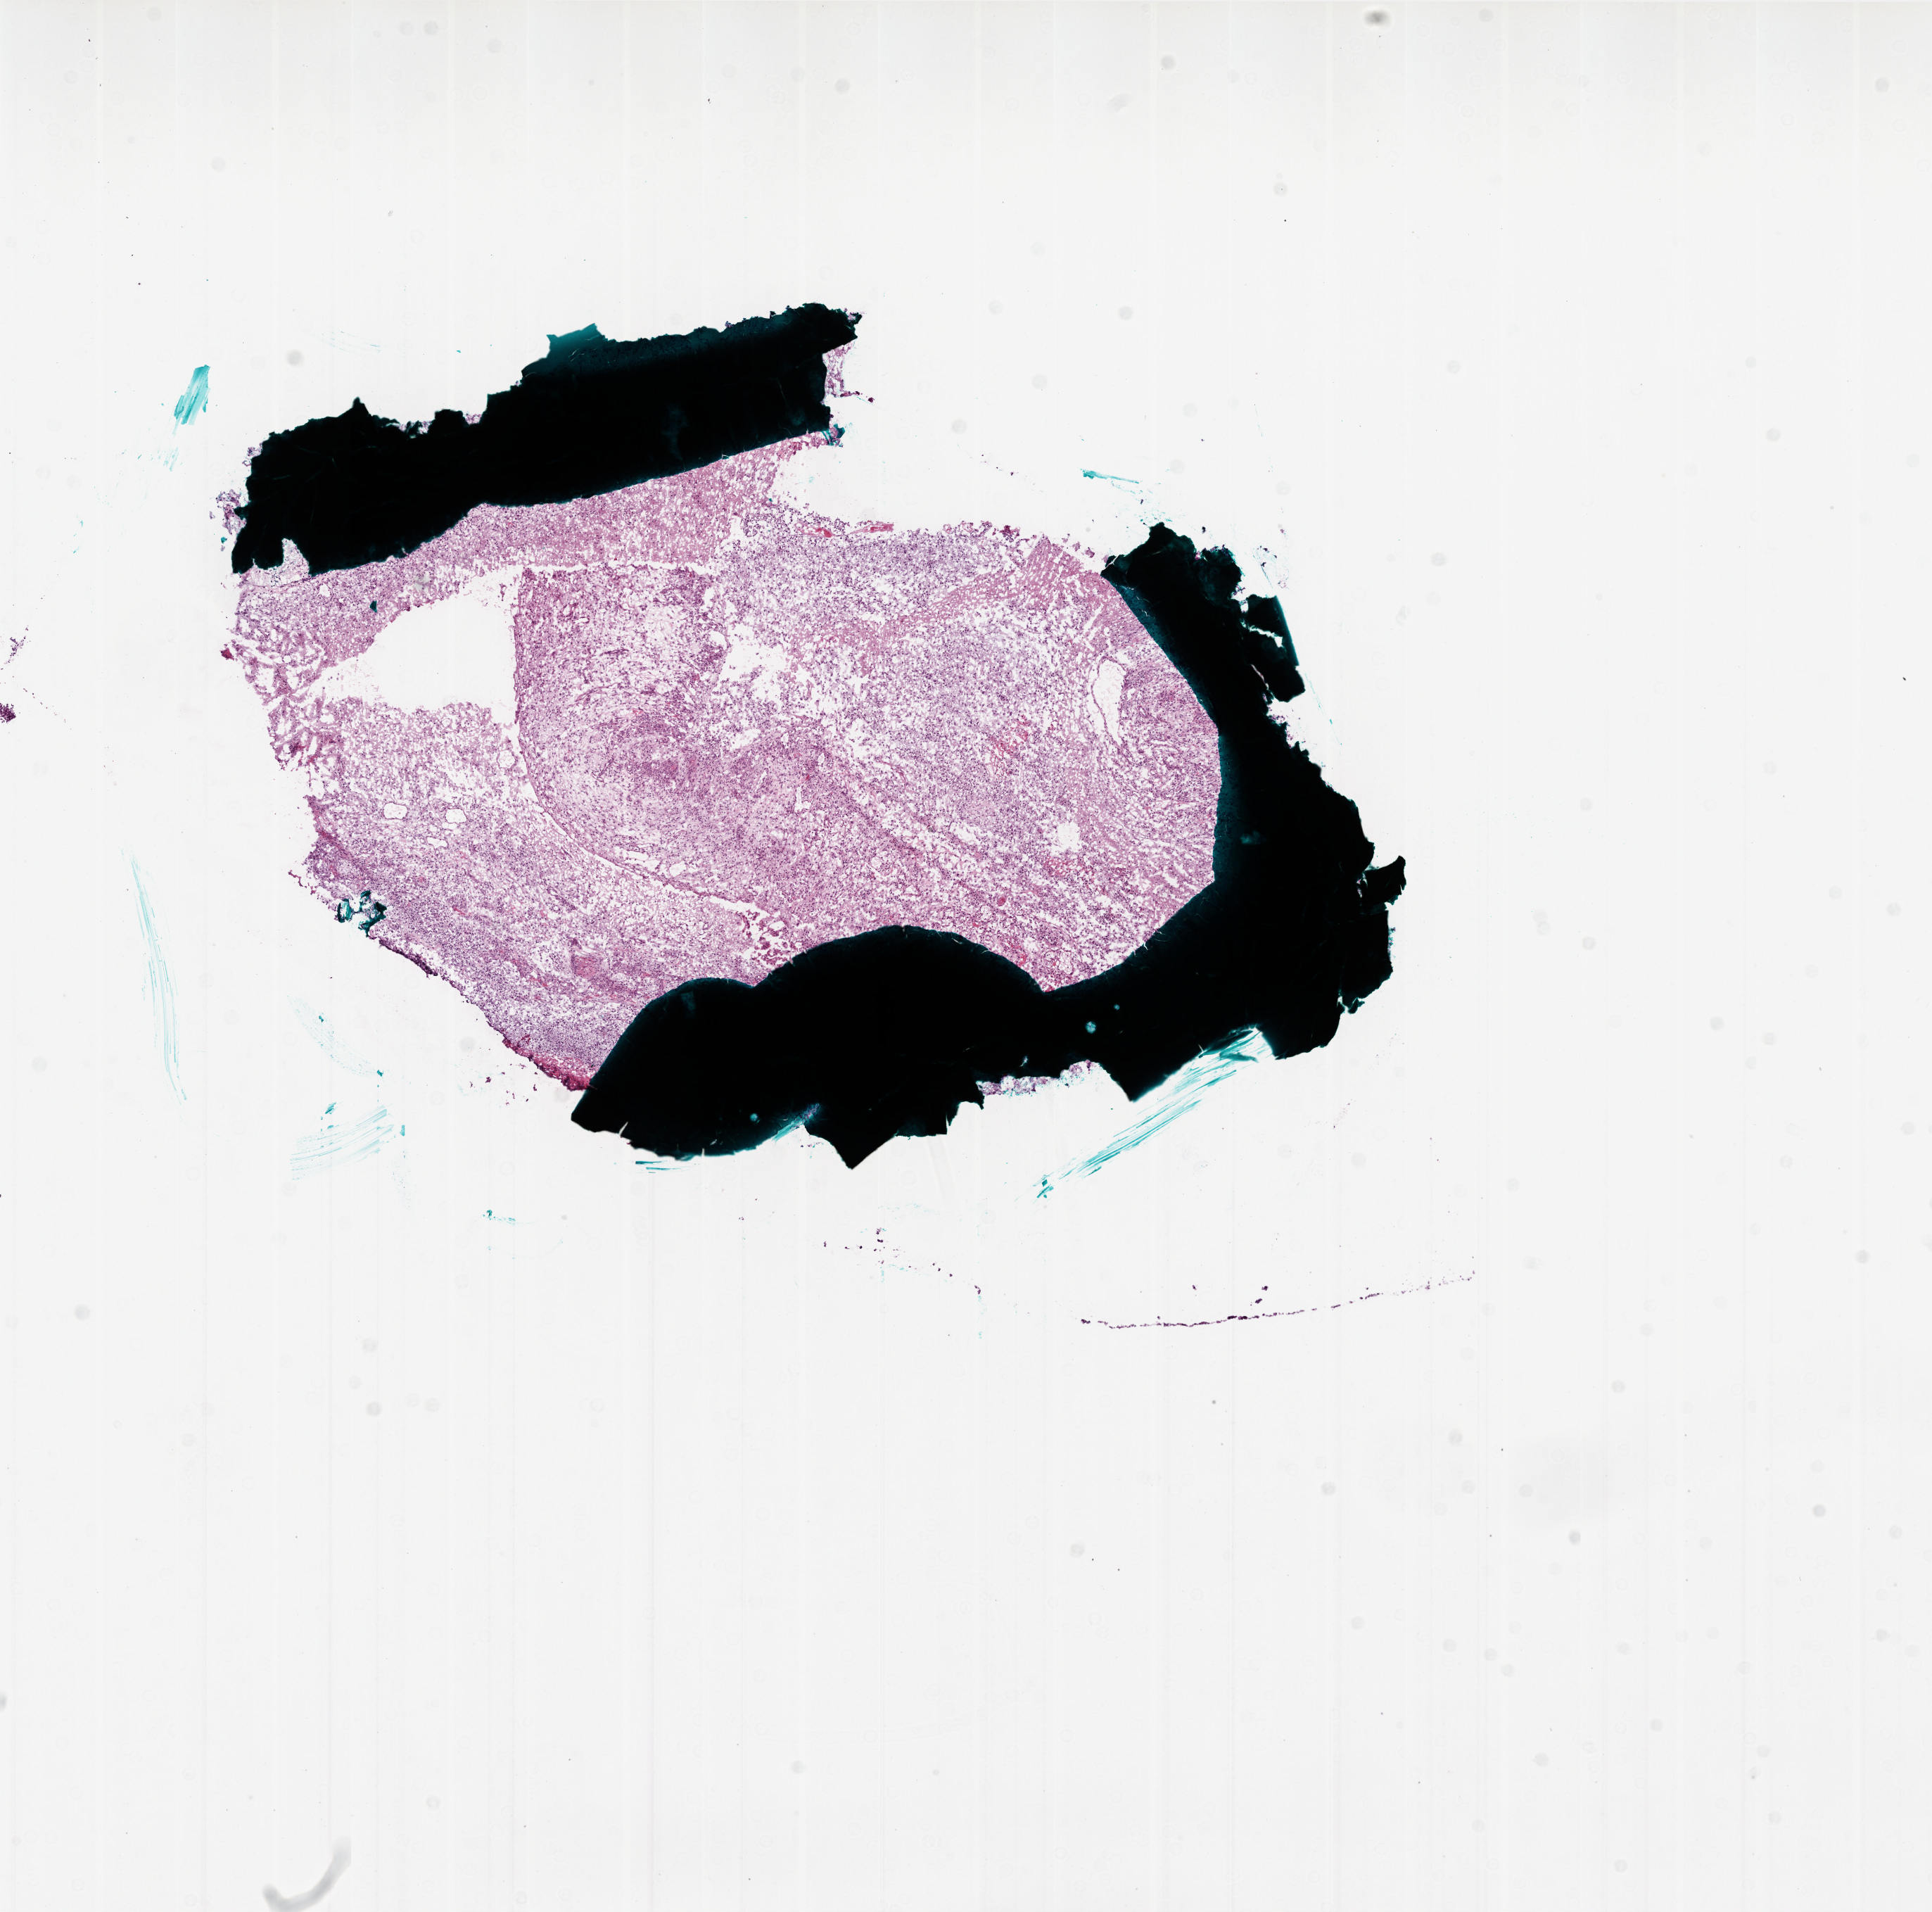
Whole-slide histology image, Hematoxylin and eosin (H&E) stained — a low-resolution overview of the entire scanned area, about 11.0 x 10.9 mm (acquisition: 20x scan), frozen section, primary tumour sample from the brain. Patient: male, age at initial diagnosis 47 years.
Histologic diagnosis: Glioblastoma.